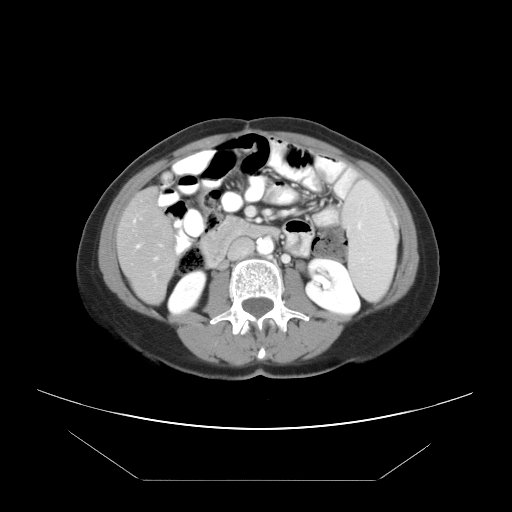
Contrast-enhanced abdominal CT, one axial slice. Position 13 of 45 along the scan axis. Reconstruction kernel STANDARD. Intravenous contrast given. Soft-tissue window (W 400 / L 40 HU). 5 mm slice thickness. 512 × 512 image matrix, field of view 405 × 405 mm. Female patient, age 52 years. From the clinical record (not read from this slice): diagnosis: colorectal cancer liver metastases, imaged before liver resection; multiple liver metastases: yes.
Annotated regions visible in this slice (expert manual segmentation):
- hepatic veins: bounding box <136,245,140,248> (left, top, right, bottom; pixels)
- liver: <118,191,175,303>
- planned liver remnant (the part of the liver to remain after resection): <118,191,172,246>
- portal vein (with intrahepatic branches): <153,256,159,261>